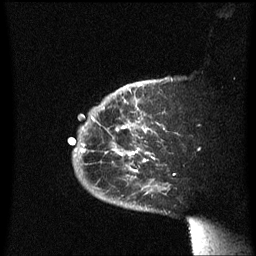
Breast MRI (dynamic contrast-enhanced), one sagittal slice; position 49 of 60 along the scan axis; dynamic contrast-enhanced series, image 2 of 3 at this slice position (ordered by acquisition); 1.5 T; TE 4.2 ms, TR 8.4 ms; 2.3 mm slice thickness; 256 × 256 image matrix. Female patient, age 38 years. Case-level facts recorded for this patient, not image findings: setting: breast cancer imaged before/during neoadjuvant chemotherapy; receptor status: HER2-positive.
Structures marked on this image (semi-automatically segmented with operator editing):
- analysis volume of interest (the breast-tissue region the enhancement analysis was run in; not a lesion): box from (x=68, y=78) to (x=176, y=213) px
- tumour enhancement mask (voxels above the 70 % enhancement threshold inside the analysis volume of interest): (x=81, y=118)–(x=148, y=173)